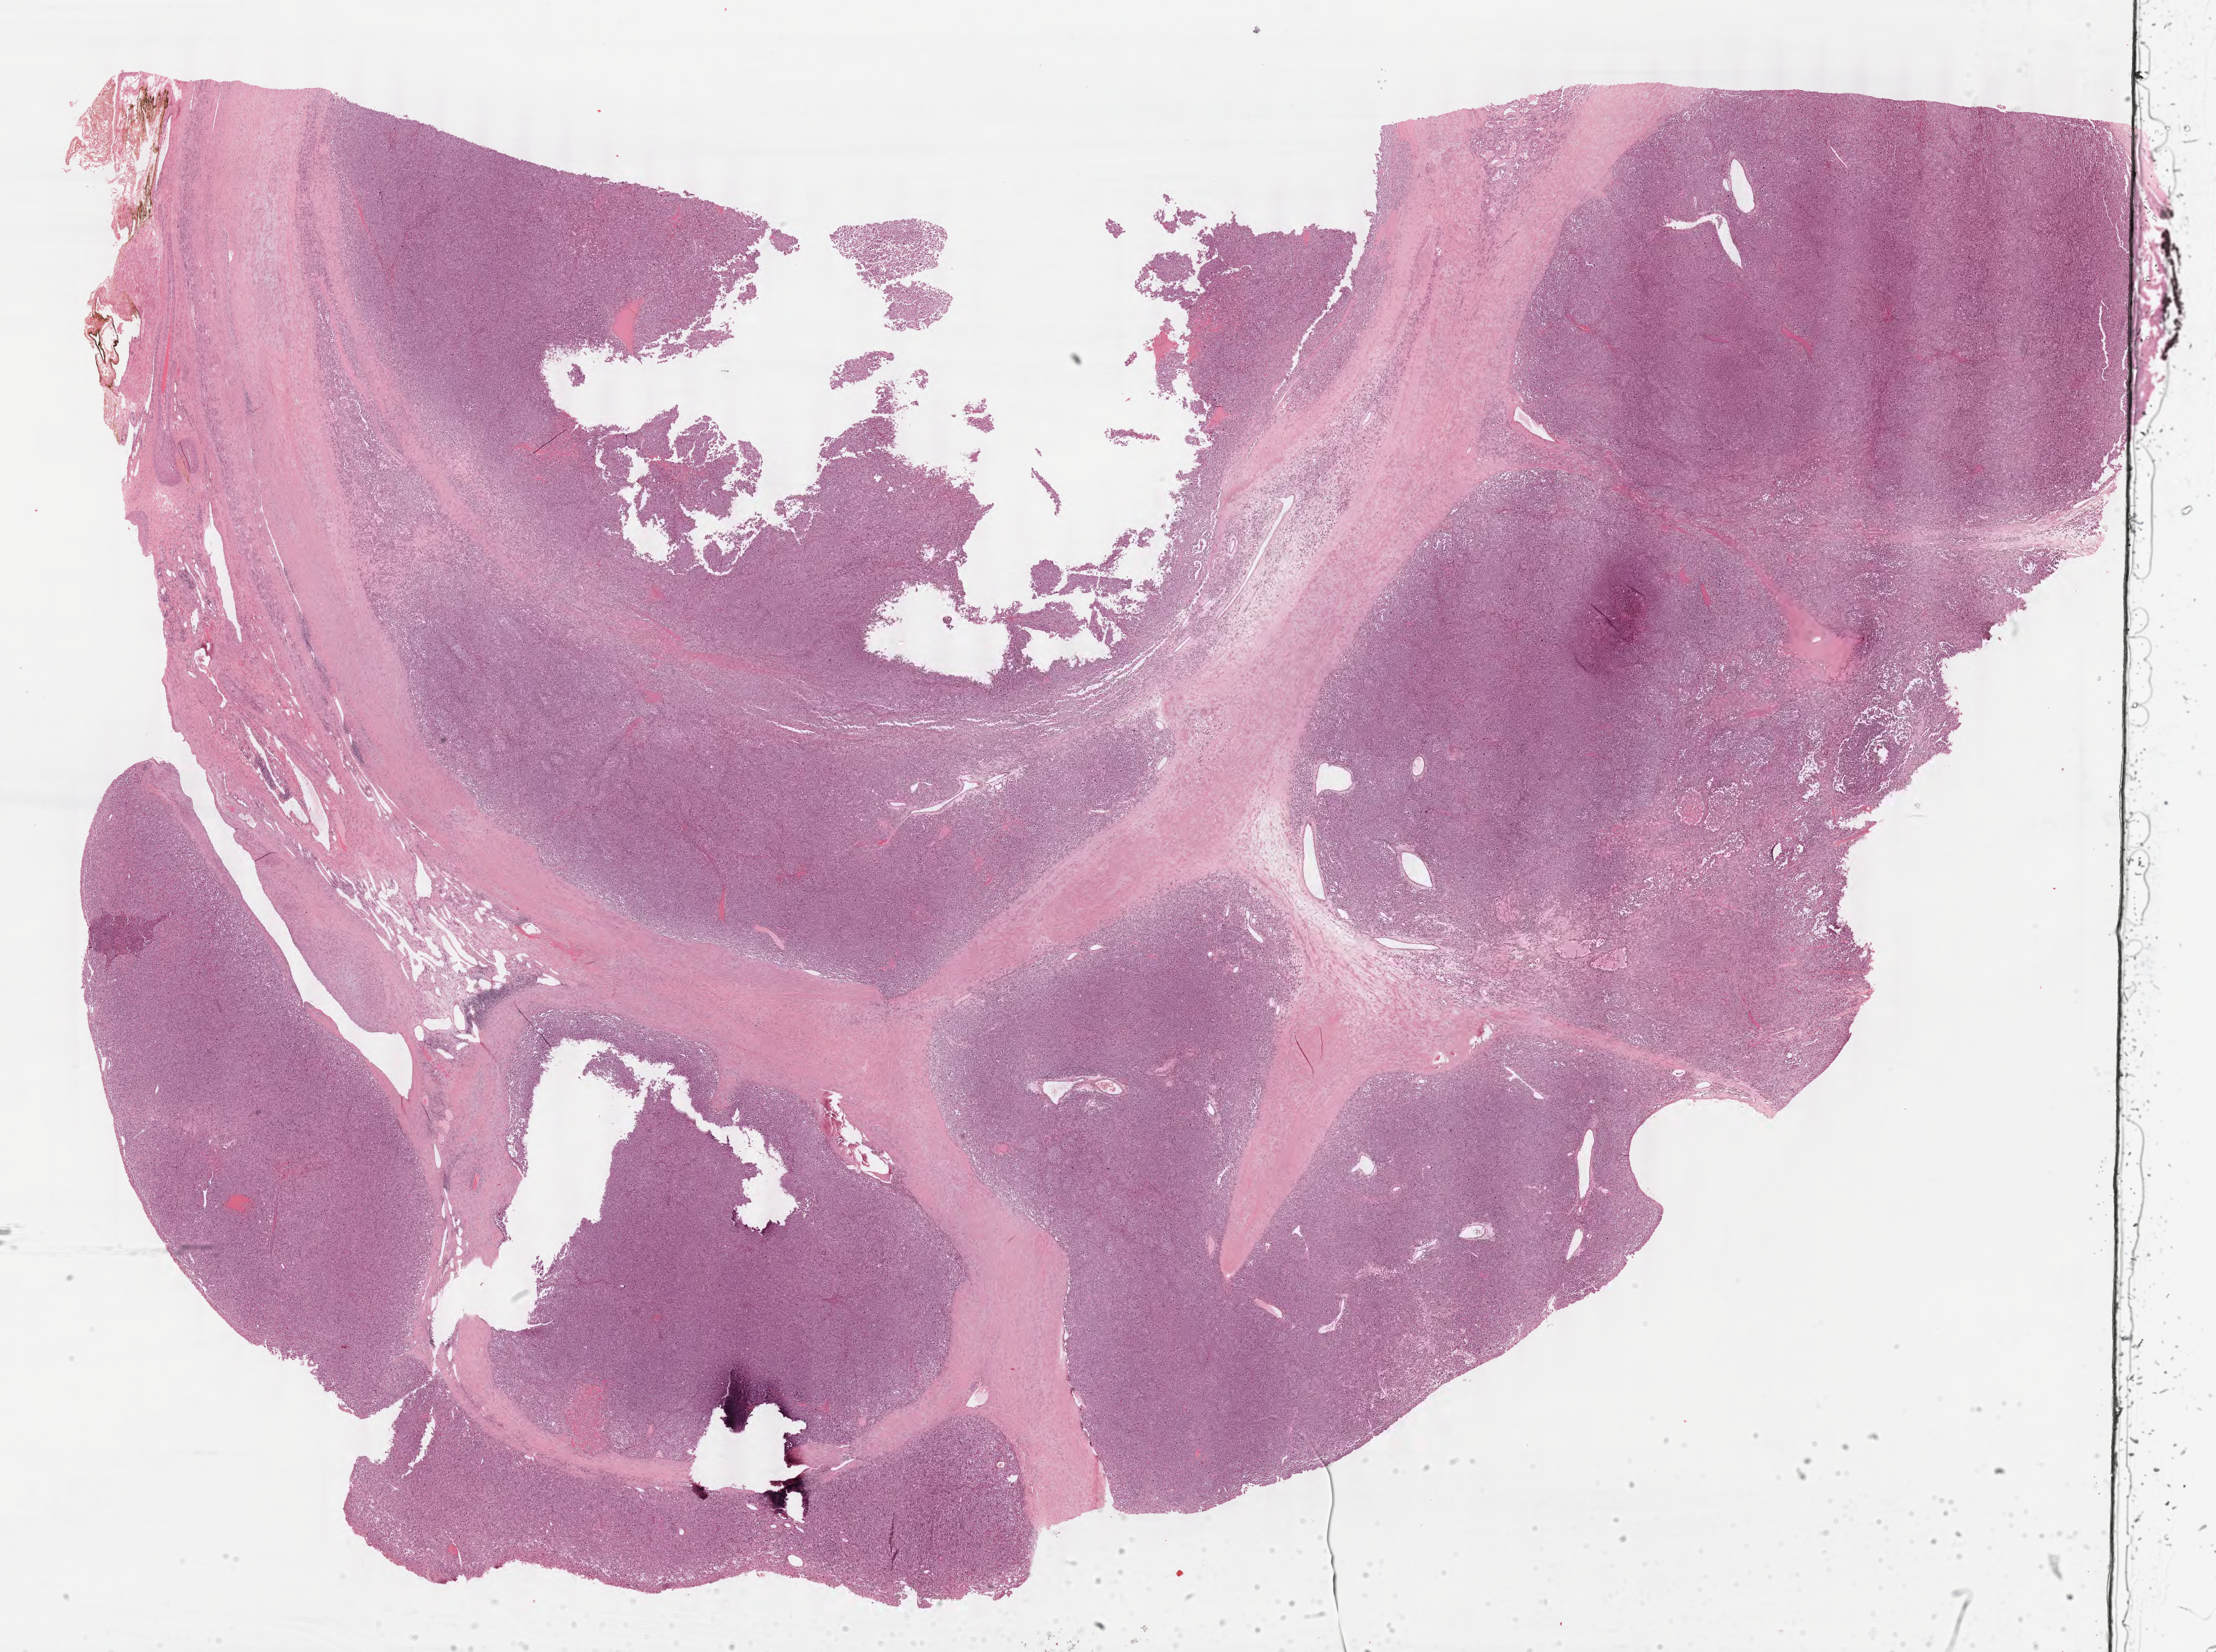
Digitized H&E tissue section (whole slide) — a low-resolution overview of the entire scanned area, about 26.1 x 19.4 mm (acquisition: 40x scan). FFPE section. Adrenal cortex, primary tumour sample. Male patient; age at initial diagnosis 63 years.
* lymph nodes positive (case pathology): 0 of 1 examined
* histologic diagnosis: Adrenal cortical carcinoma (cortex of adrenal gland)